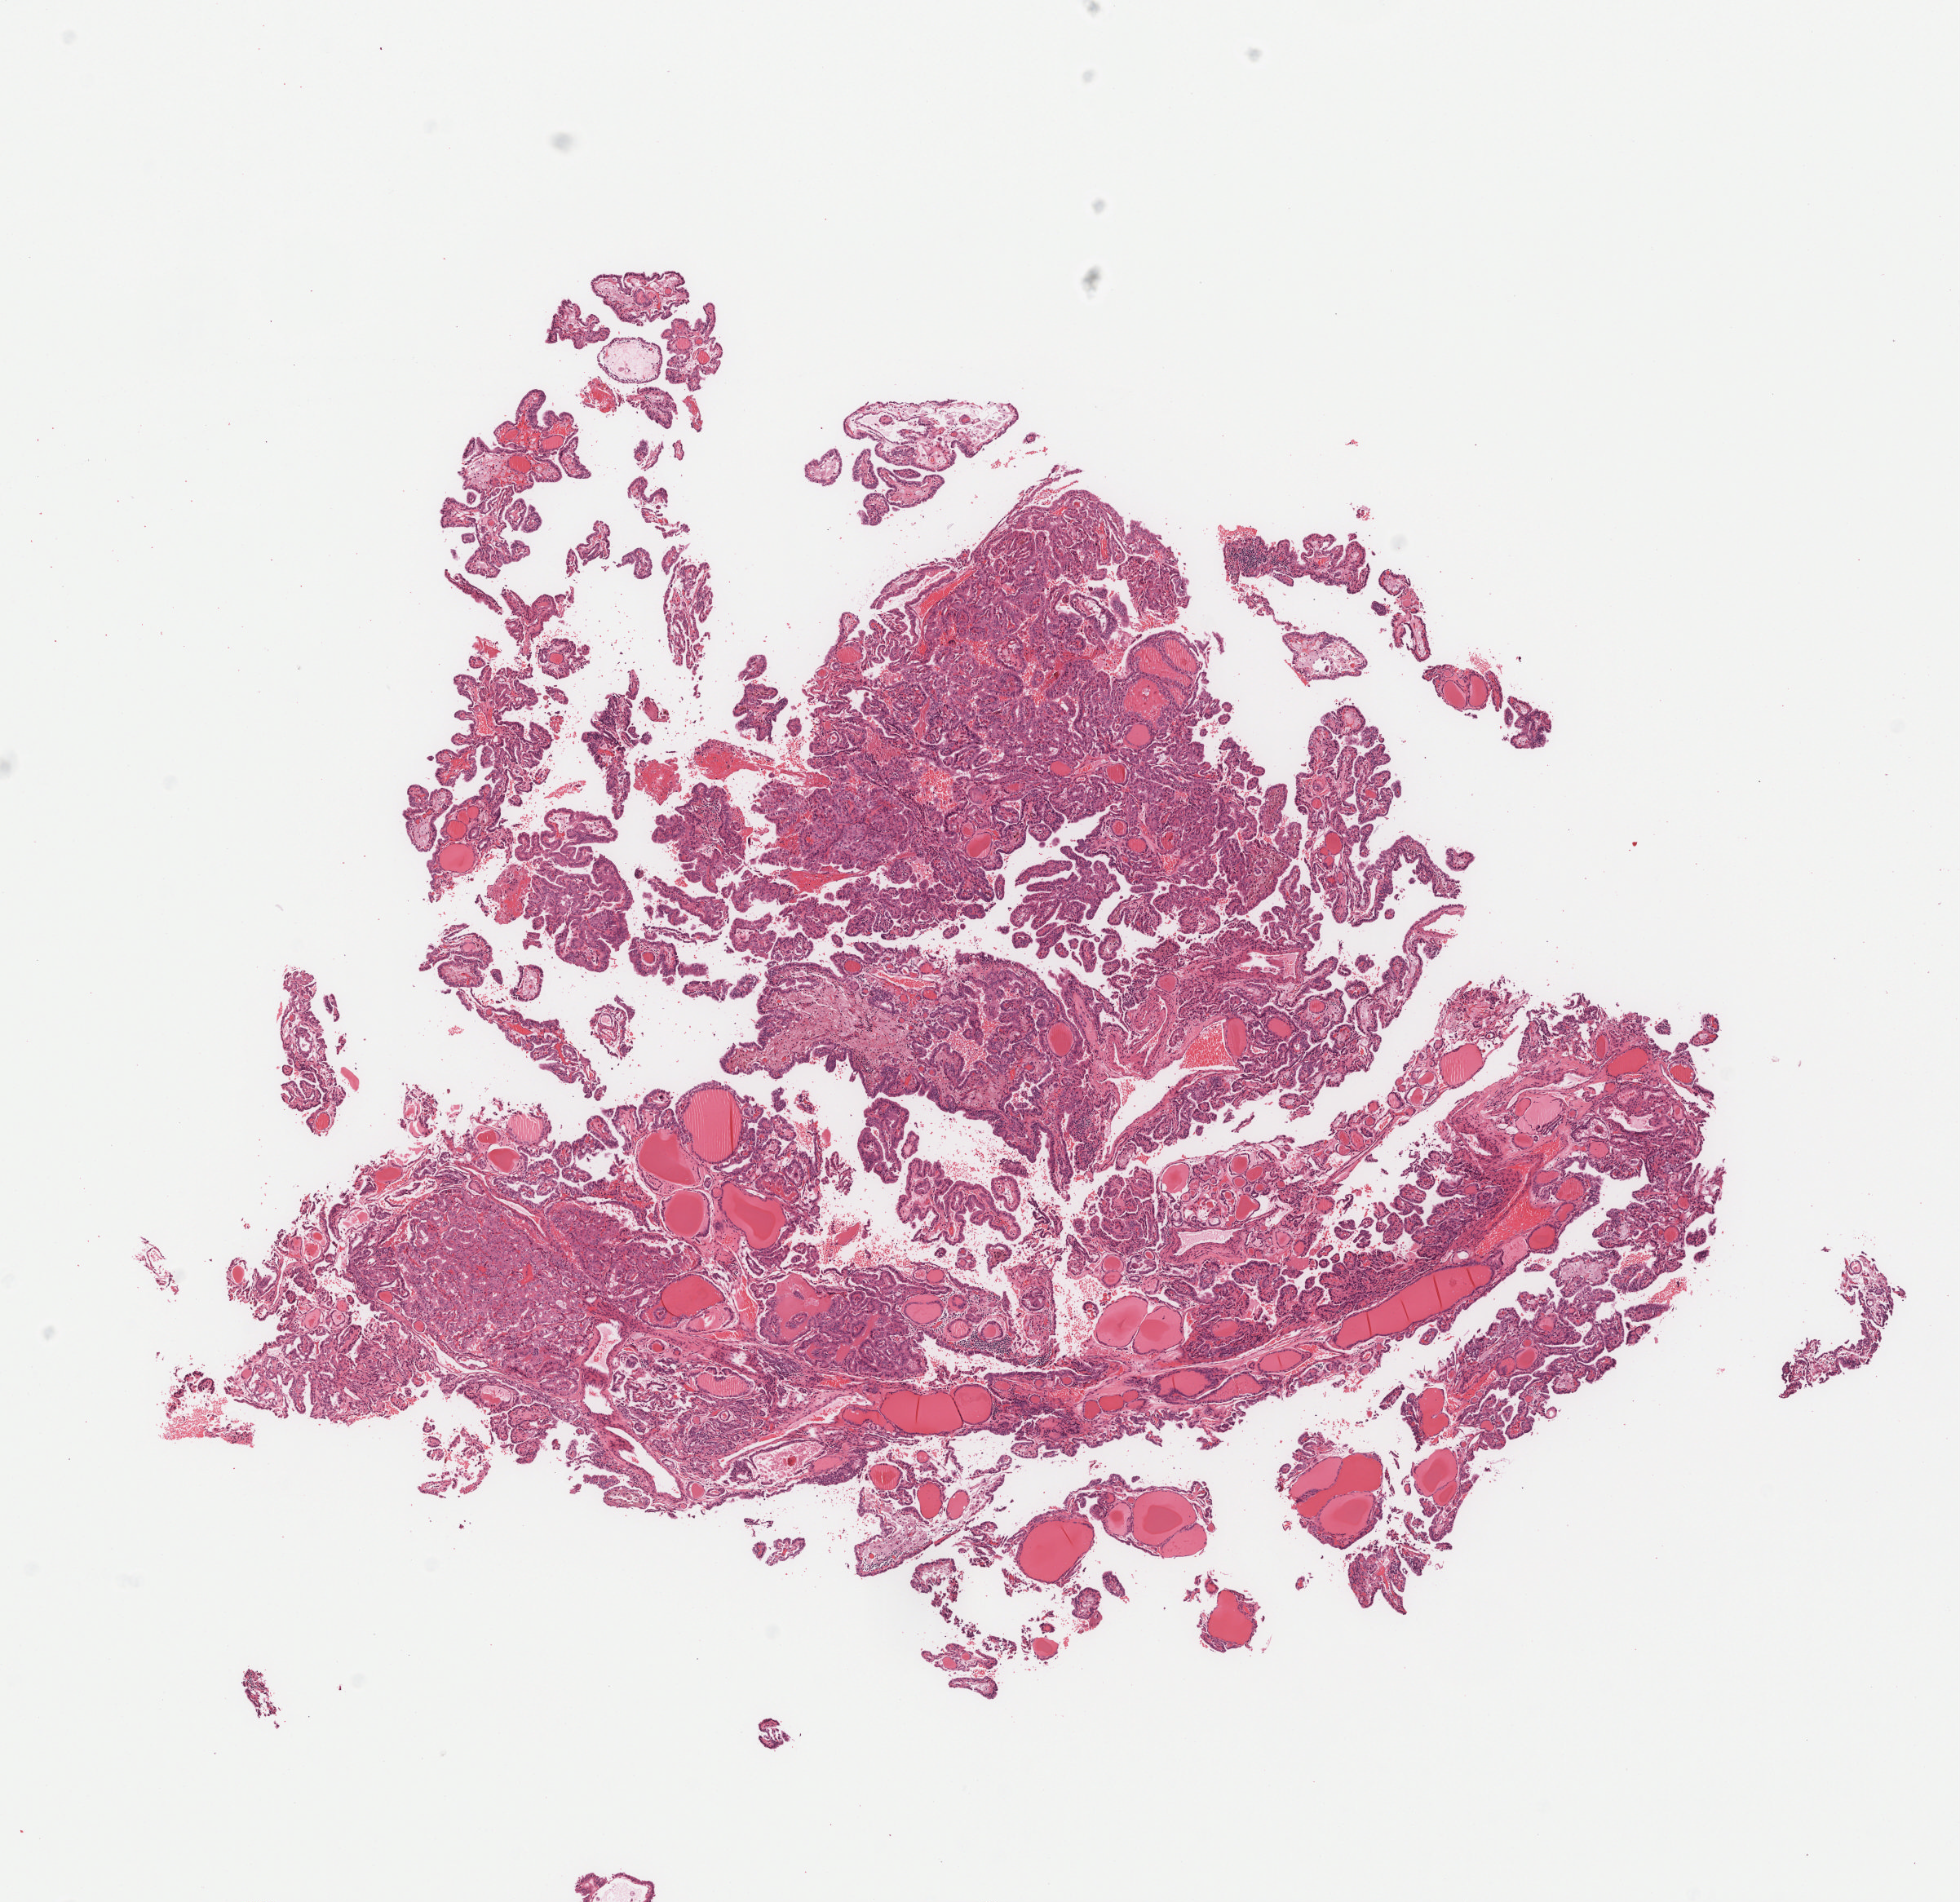
Hematoxylin and eosin (H&E) stained whole-slide image, a low-resolution overview of the entire scanned area, about 9.7 x 9.4 mm (acquisition: 40x scan); FFPE section; sample: primary tumour, thyroid. Female patient; age at initial diagnosis 62 years.
Diagnosis: Papillary adenocarcinoma, NOS (thyroid gland). TNM: T1b N0 MX. AJCC pathologic stage: I.